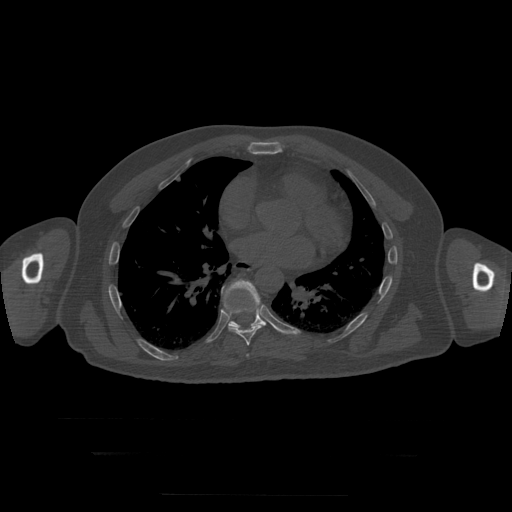
CT including the spine, one axial slice. Position 158 of 397 along the scan axis. 120 kVp. Bone window (W 1800 / L 400 HU). 512 × 512 image matrix, field of view 510 × 510 mm. Patient age 73 years. From the clinical record (not read from this slice): primary cancer: prostate.
Structures marked on this image (semi-automatic segmentation, software-assisted and operator-edited):
- T7 vertebra: bounding box (x1, y1, x2, y2) in pixels: (247, 355, 249, 357)
- T8 vertebra: (222, 287, 266, 346)
- T9 vertebra: (224, 280, 265, 329)